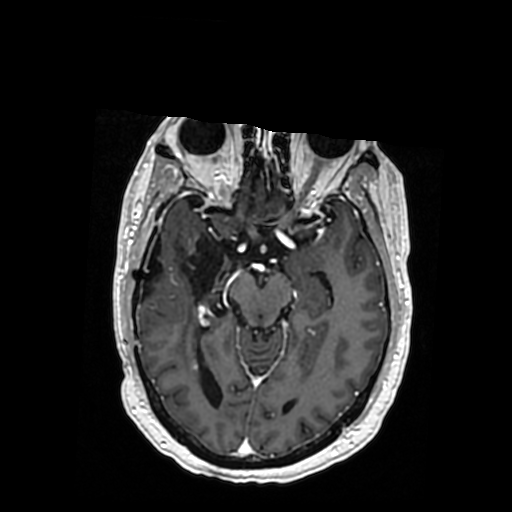
Brain MRI from a brain-tumour surgery series, one axial slice; slice 211 of 364 in the series (ordered by position); T1-weighted post-contrast; 0.5 mm slice thickness; 512 × 512 image matrix, field of view 260 × 260 mm. From the clinical record (not read from this slice): histopathology: Oligodendroglioma; WHO grade: 3; IDH mutation: yes; tumour location: Right Posterior Temporal Inferior Parietal.
Structures marked on this image (outlined manually by an expert reader):
- previous resection cavity: bounding box [x1, y1, x2, y2] px = [143, 232, 237, 301]